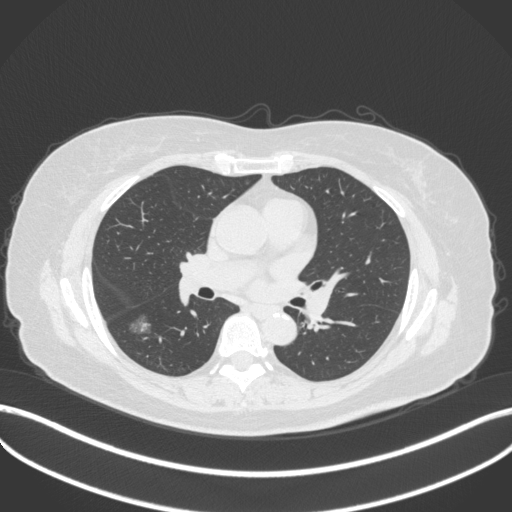
Chest CT, one axial slice. Position 172 of 322 along the scan axis. Reconstruction kernel B31f. 120 kVp. Lung window (W 1500 / L -600 HU). 1 mm slice thickness. 512 × 512 image matrix, field of view 400 × 400 mm. Patient: female, 64 years. Case-level facts recorded for this patient, not image findings: clinical TNM (as recorded): T1c N0 M0.
Structures marked on this image (rectangle marked by the reading radiologist):
- lung tumour (recorded histology: adenocarcinoma): bounding box <130,313,155,337> (left, top, right, bottom; pixels)